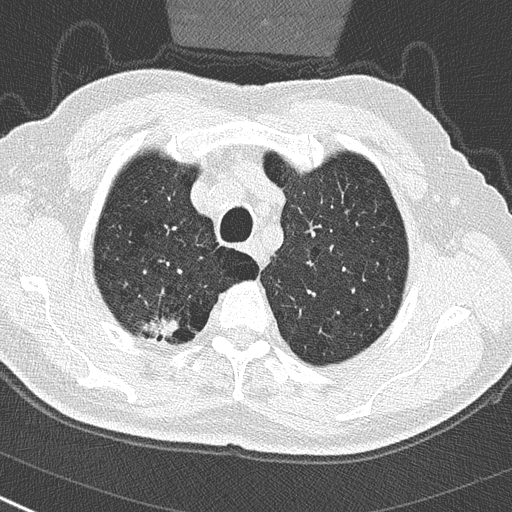
Low-dose screening chest CT, one axial slice; slice 241 of 290 in the series (ordered by position); reconstruction kernel B50f; 120 kVp; lung window (W 1500 / L -600 HU); 2 mm slice thickness; 512 × 512 image matrix, field of view 300 × 300 mm.
Annotated regions visible in this slice (expert manual segmentation):
- lesion 1 (tumor, upper lobe of right lung): bounding box (x1, y1, x2, y2) in pixels: (142, 316, 179, 338)